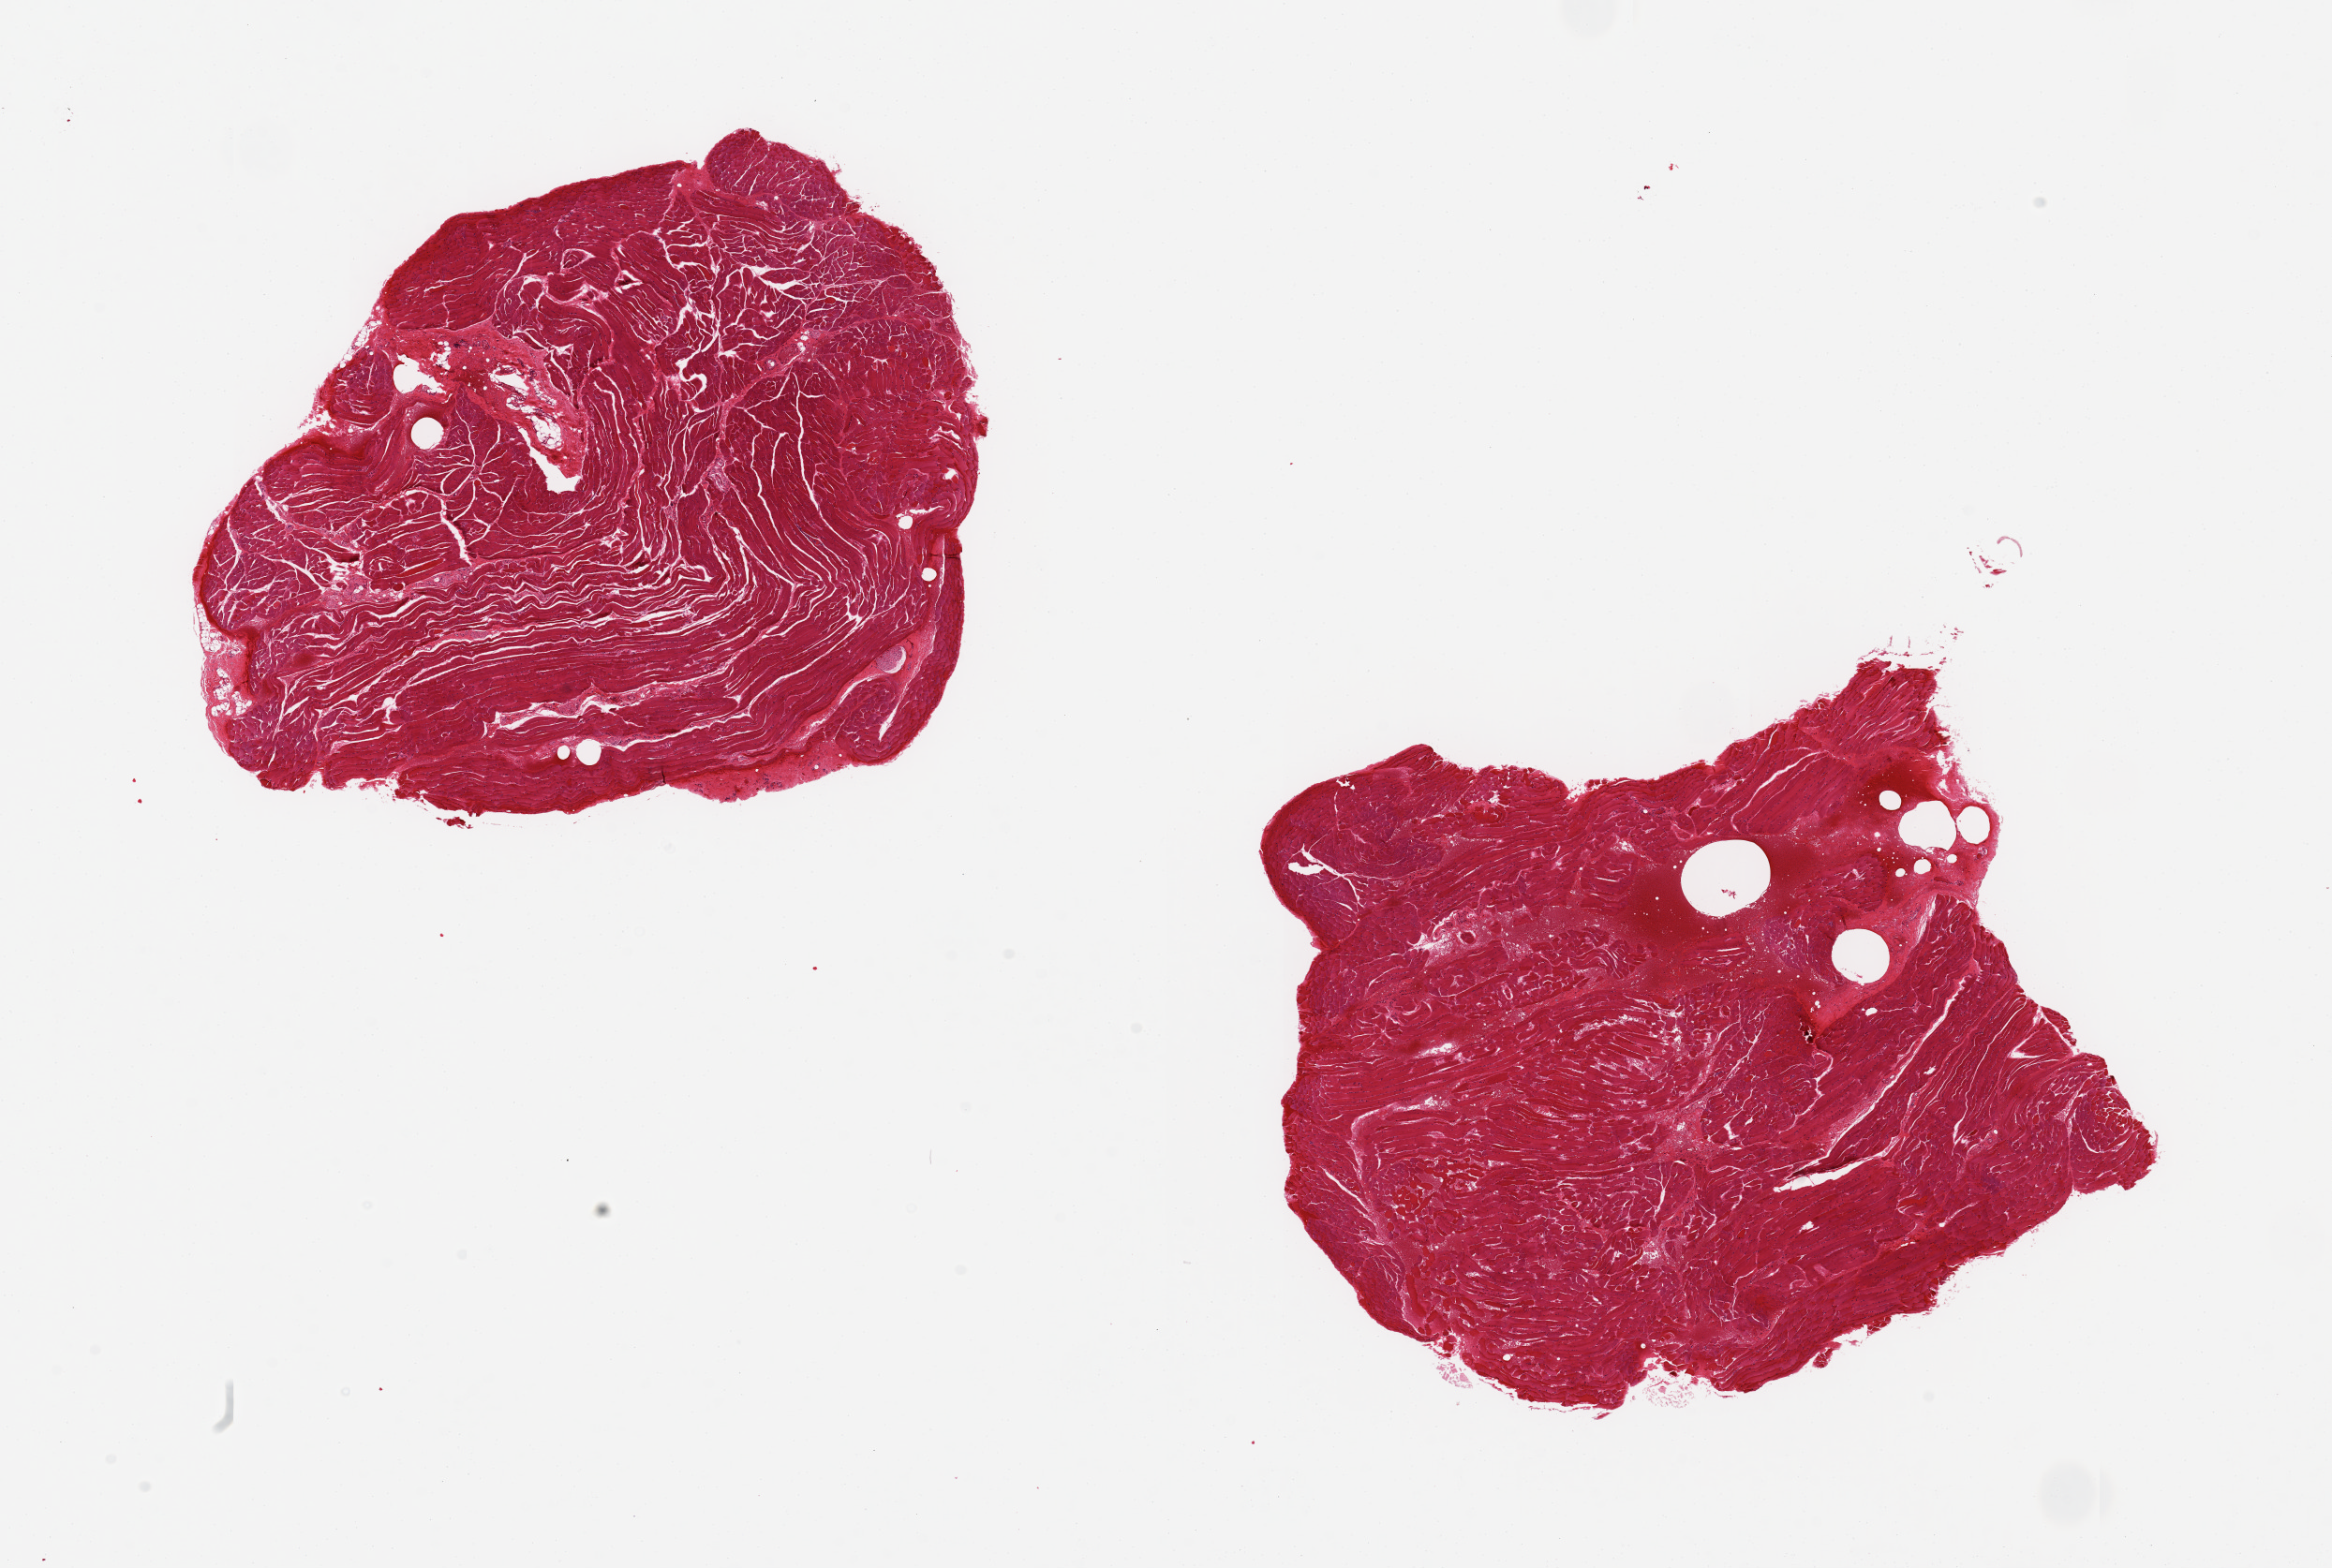
Whole-slide image, H&E stain, whole scanned area (about 19.7 x 13.2 mm, from a 20x scan) shown as a low-resolution overview, PAXgene-fixed paraffin-embedded (PFPE) section, sampled site (target tissue): thyroid, donor tissue sample.
Reviewer comment on this tissue sample: 2 pieces 6x6 & 6x5 mm; NO THYROID; only skeletal muscle.